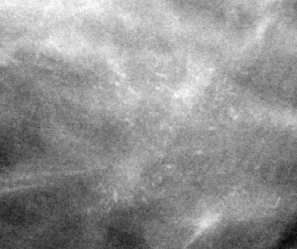
Crop from a digitized film mammogram around one marked abnormality, left breast, CC view.
- Marked abnormality: calcifications, morphology pleomorphic / fine linear branching, distribution clustered; BI-RADS assessment category 4; subtlety rating 2 on a 1 (subtle) to 5 (obvious) scale; pathology result (as recorded, not read from the image): benign.